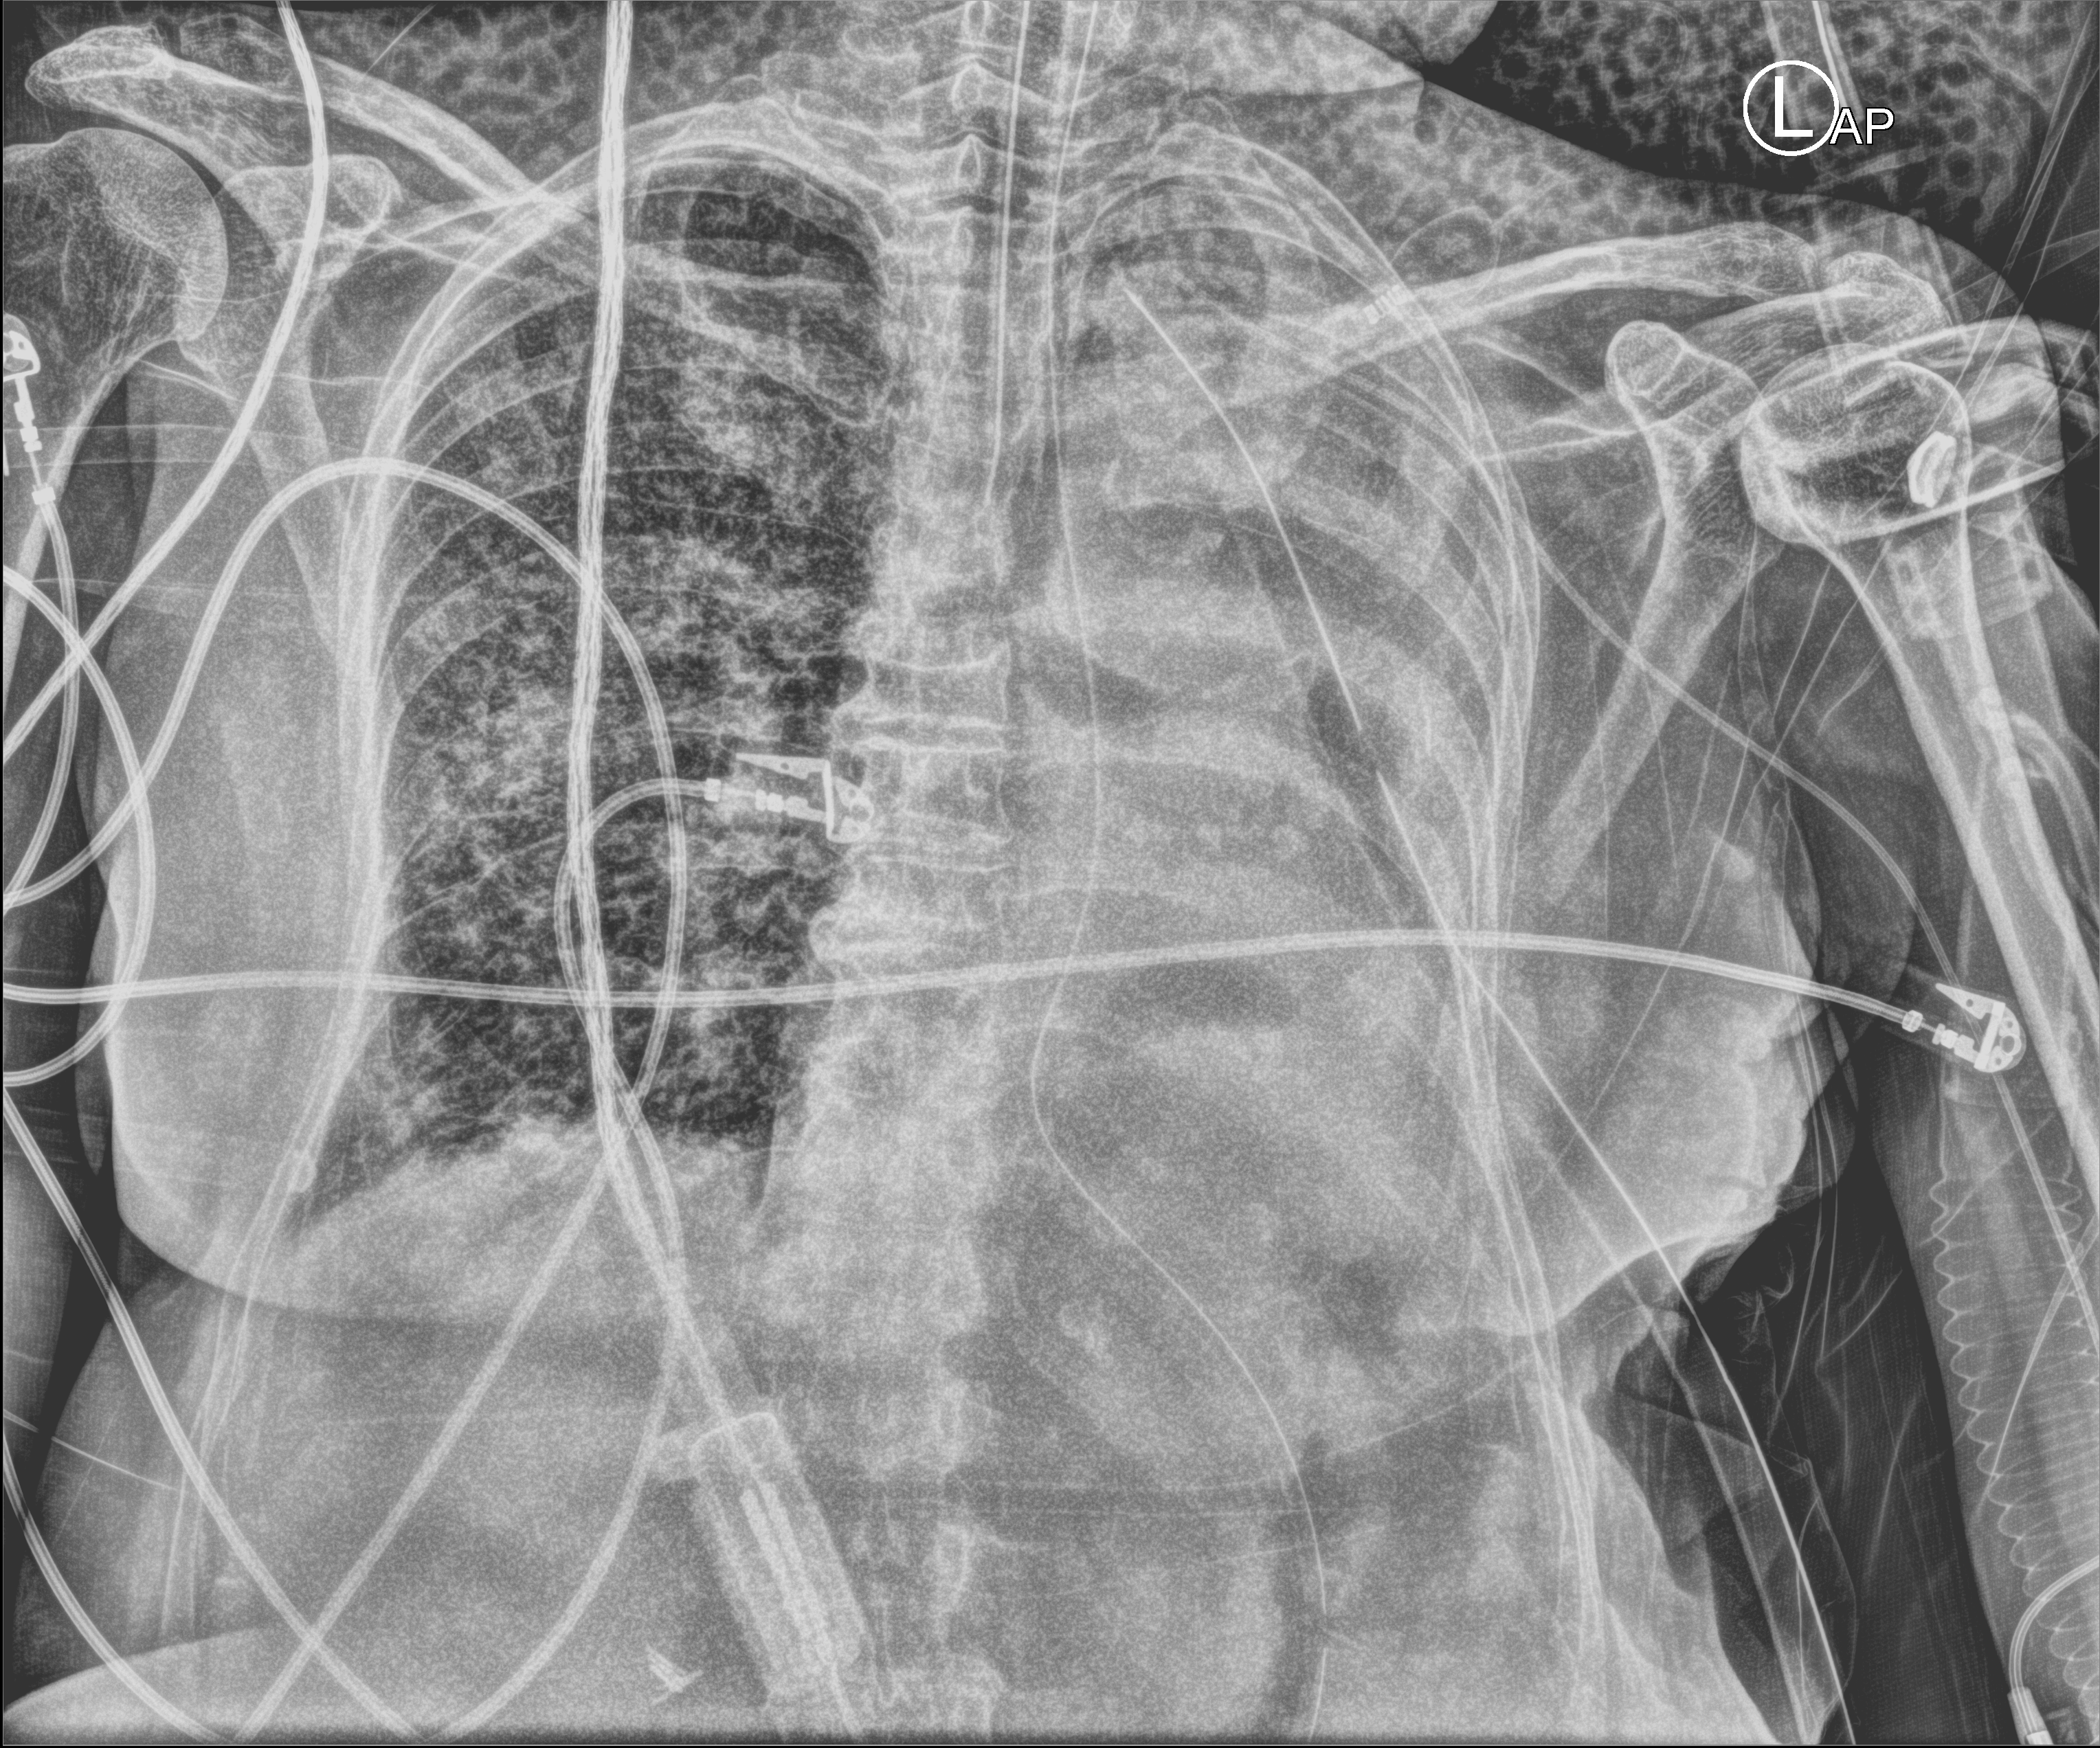
Chest X-ray (portable), anteroposterior (AP) projection. Female patient hospitalised with COVID-19, age 75–90 years.
Hospital-stay facts (about this admission, not read from this image; timing relative to this image not recorded): hypertension (admission record): yes.